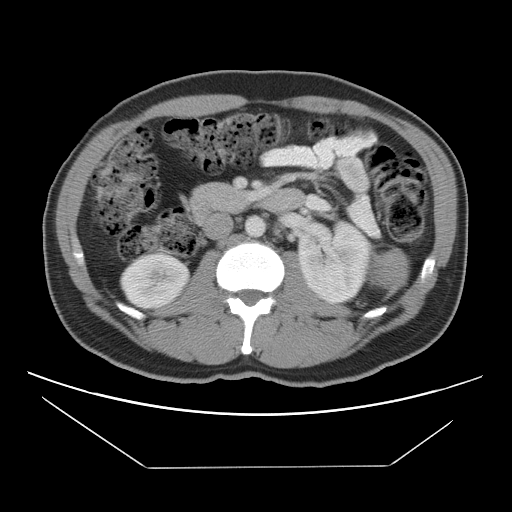
Contrast-enhanced abdominal CT, one axial slice; position 60 of 131 along the scan axis; reconstruction kernel STANDARD; intravenous contrast given; soft-tissue window (W 400 / L 40 HU); 512 × 512 image matrix, field of view 396 × 396 mm. Patient: male, 44 years. Case-level facts recorded for this patient, not image findings: diagnosis: adrenocortical carcinoma; tumour side: left adrenal; tumour size at pathology: 15.5 cm; Ki-67 index: 6 %; stage (as recorded): 2.
Outlined on this slice (semi-automatically segmented with operator editing):
- mass: bounding box <372,249,407,287> (left, top, right, bottom; pixels)